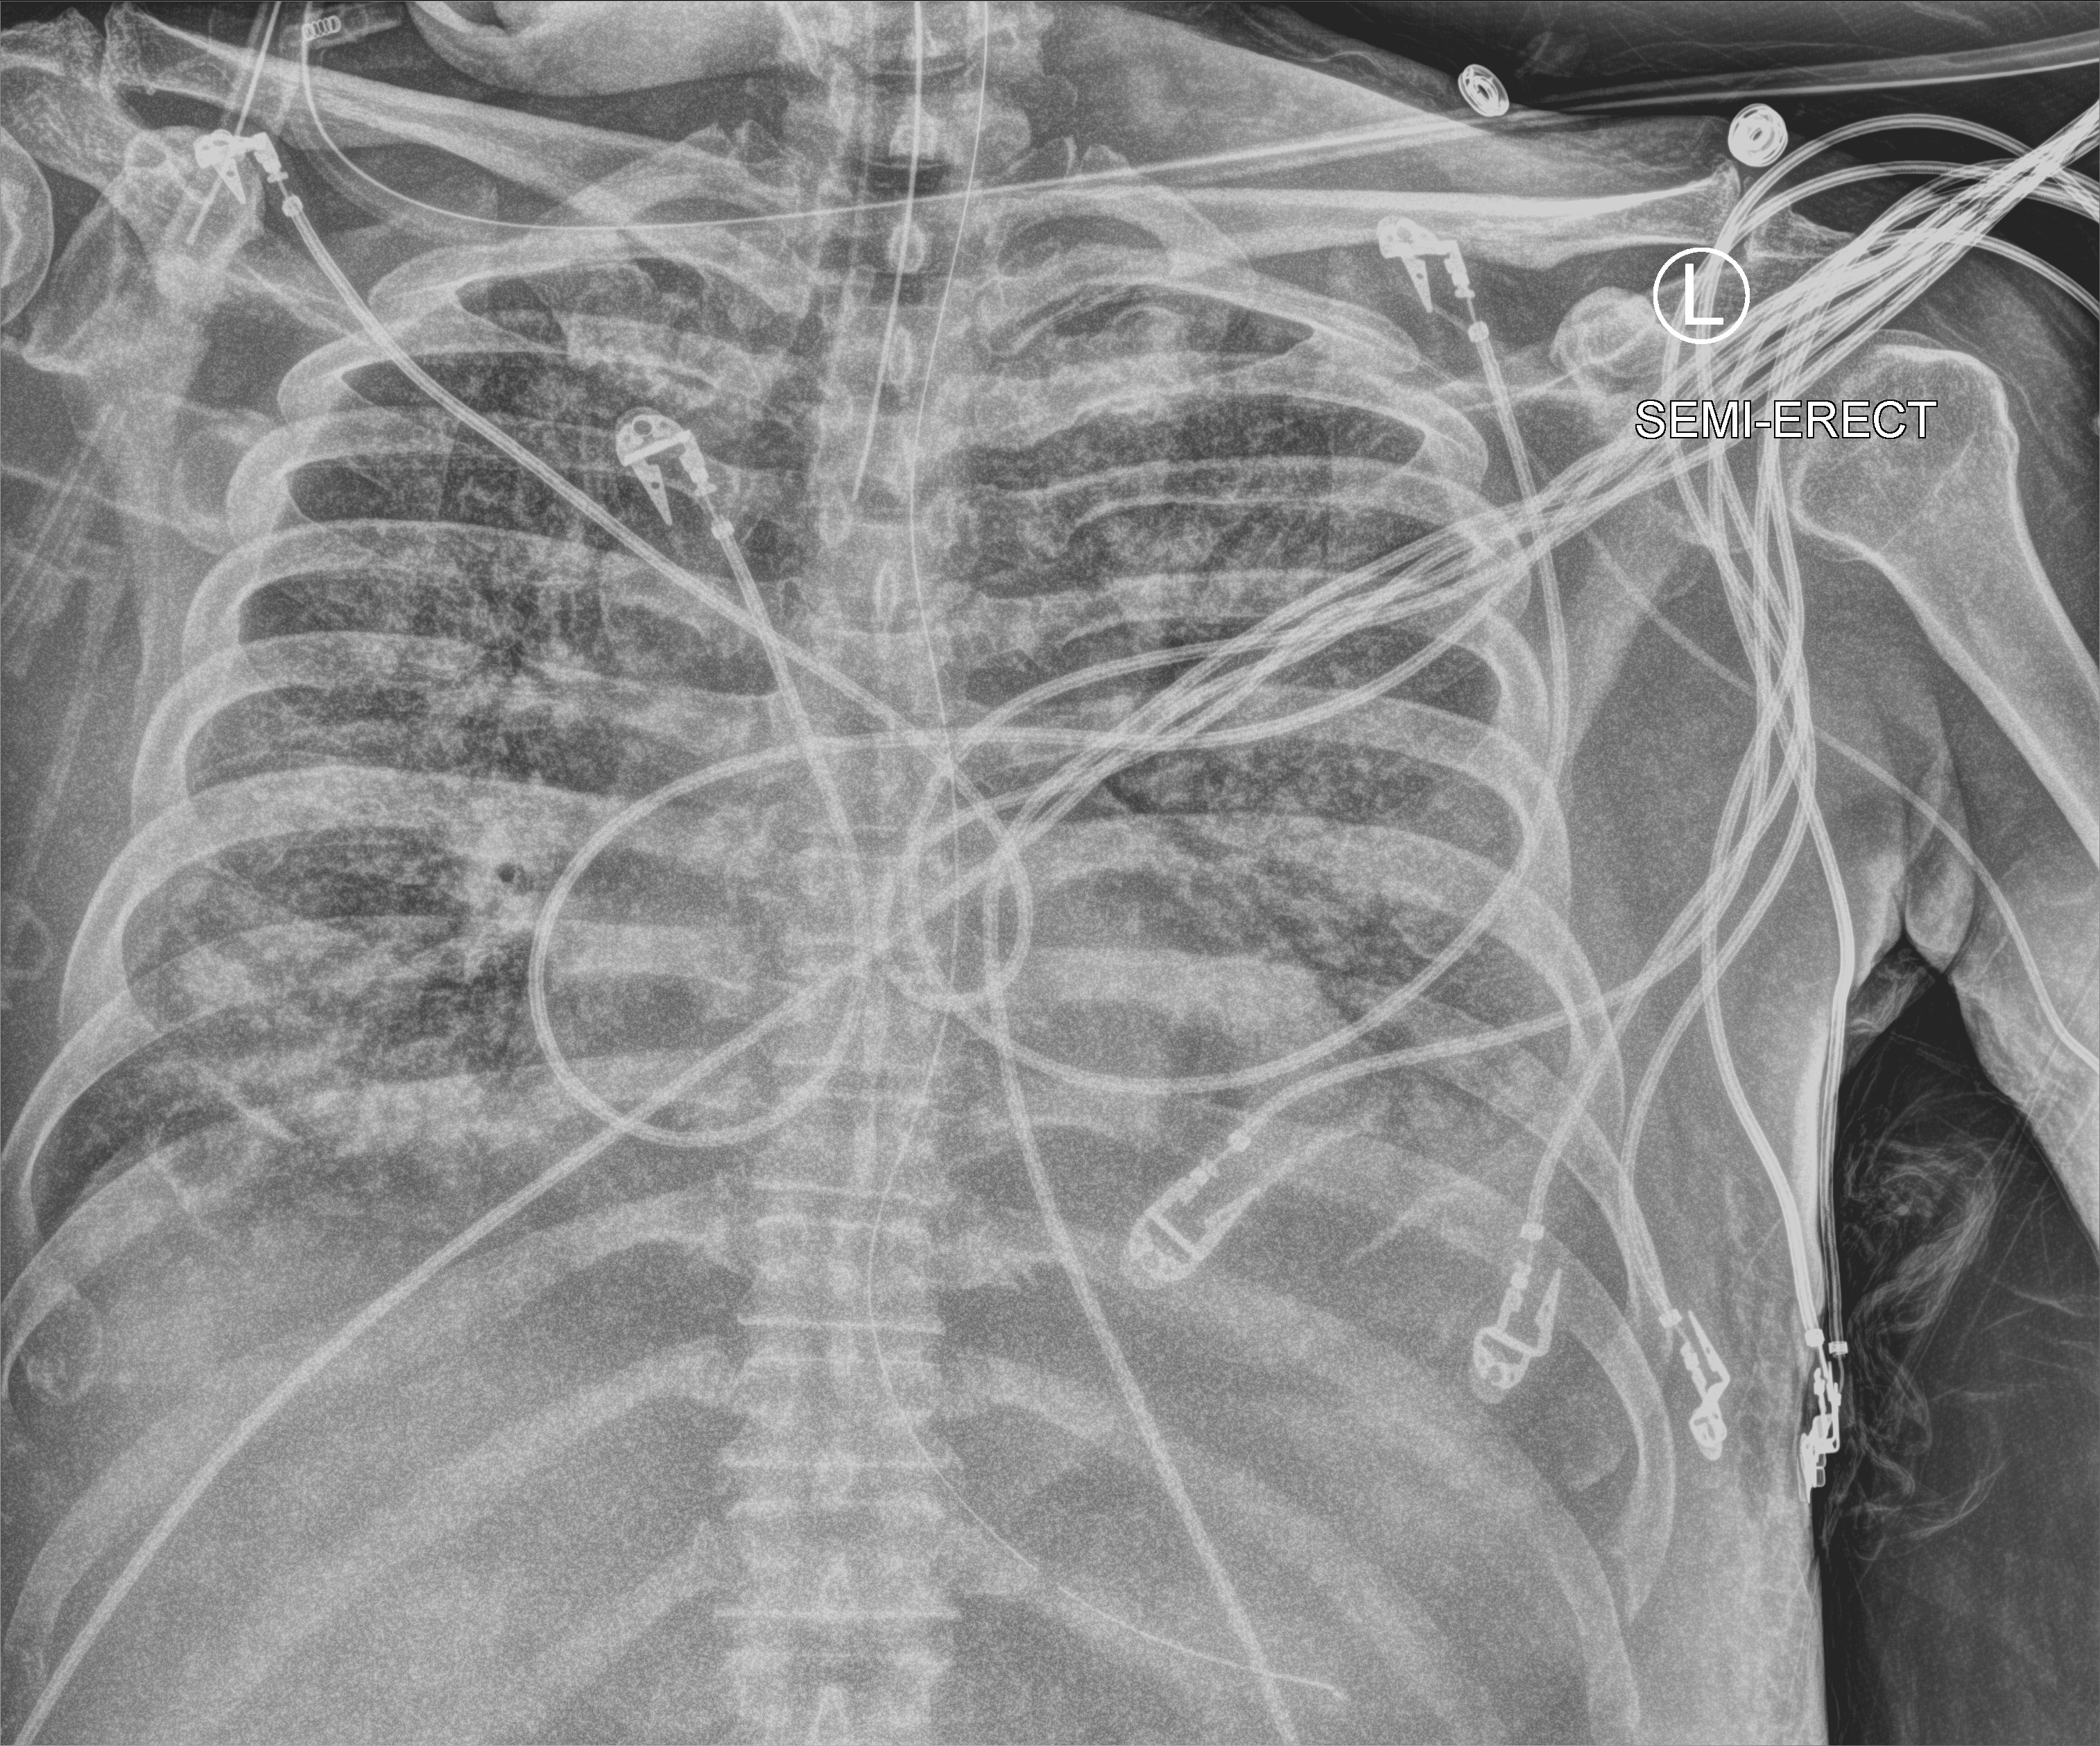
Portable chest radiograph; anteroposterior (AP) projection. Male patient hospitalised with COVID-19, age 60–74 years.
From the hospital-stay record, not from the radiograph (when in the stay this image was taken is not recorded):
- admitted to intensive care during this hospital stay: yes
- mechanically ventilated during this hospital stay: yes